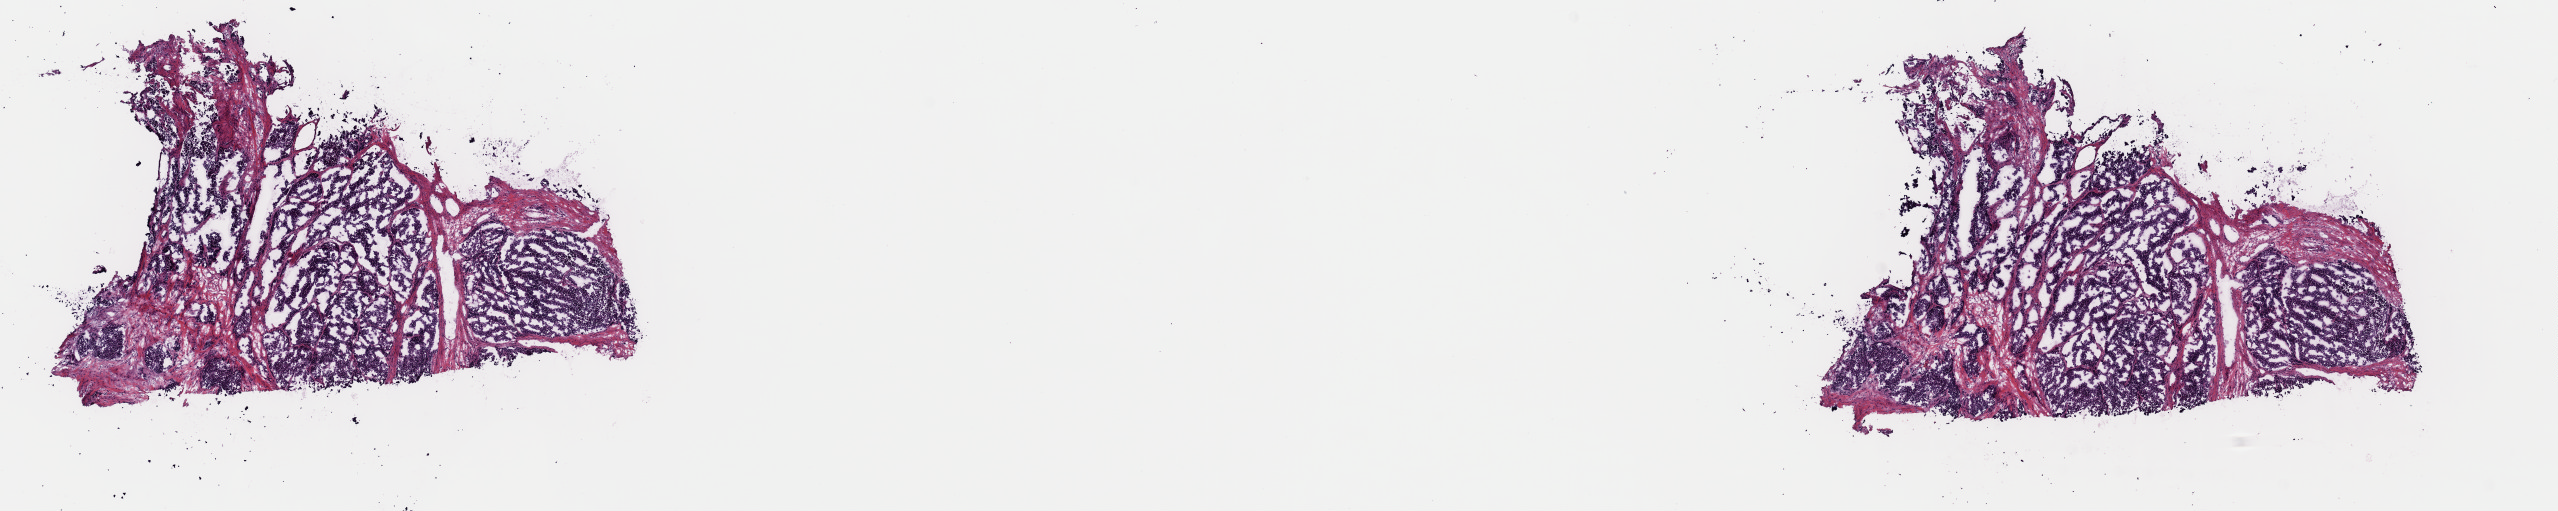
Hematoxylin and eosin (H&E) stained whole-slide image, low-resolution overview of the scanned area, about 20.2 x 4.0 mm (slide scanned at 40x), frozen section from the top of the tissue portion, skin, primary tumour sample. Male, age 76 years at initial diagnosis. Slide review estimates, as recorded: tumour cells 80%, tumour nuclei 80%, normal cells 0%, stromal cells 20%, necrosis 0%. Inflammatory infiltration, as recorded: lymphocyte infiltration 3%, monocyte infiltration 2%, neutrophil infiltration 1%.
* histologic diagnosis: Malignant melanoma, NOS